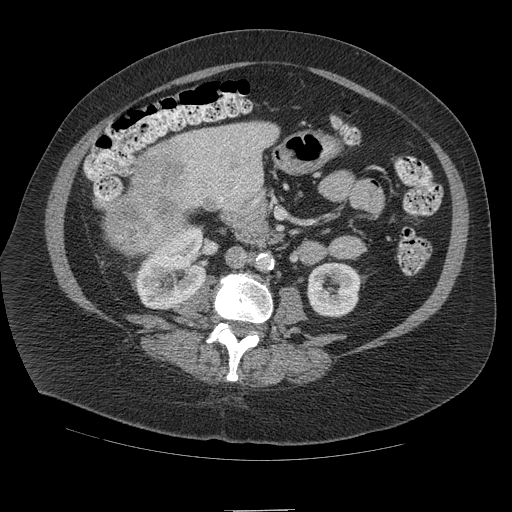
Contrast-enhanced abdominal CT (liver protocol), one axial slice; position 32 of 109 along the scan axis; reconstruction kernel STANDARD; soft-tissue window (W 400 / L 40 HU); 2.5 mm slice thickness; 512 × 512 image matrix, field of view 420 × 420 mm. From the clinical record (not read from this slice): diagnosis: hepatocellular carcinoma (patient treated with transarterial chemoembolisation; whether this scan precedes or follows treatment is not stated here); TNM stage (as recorded): Stage-IVB; Child-Pugh class: A; tumour differentiation: poorly differentiated; tumour nodularity: multinodular.
Annotated regions visible in this slice (semi-automatic segmentation, software-assisted and operator-edited):
- liver parenchyma outside the tumour (the mass and vessels are separate outlines, so this box may not span the whole liver): bounding box <116,122,279,234> (left, top, right, bottom; pixels)
- mass: <100,146,189,255>
- liver vessels: <190,132,258,202>